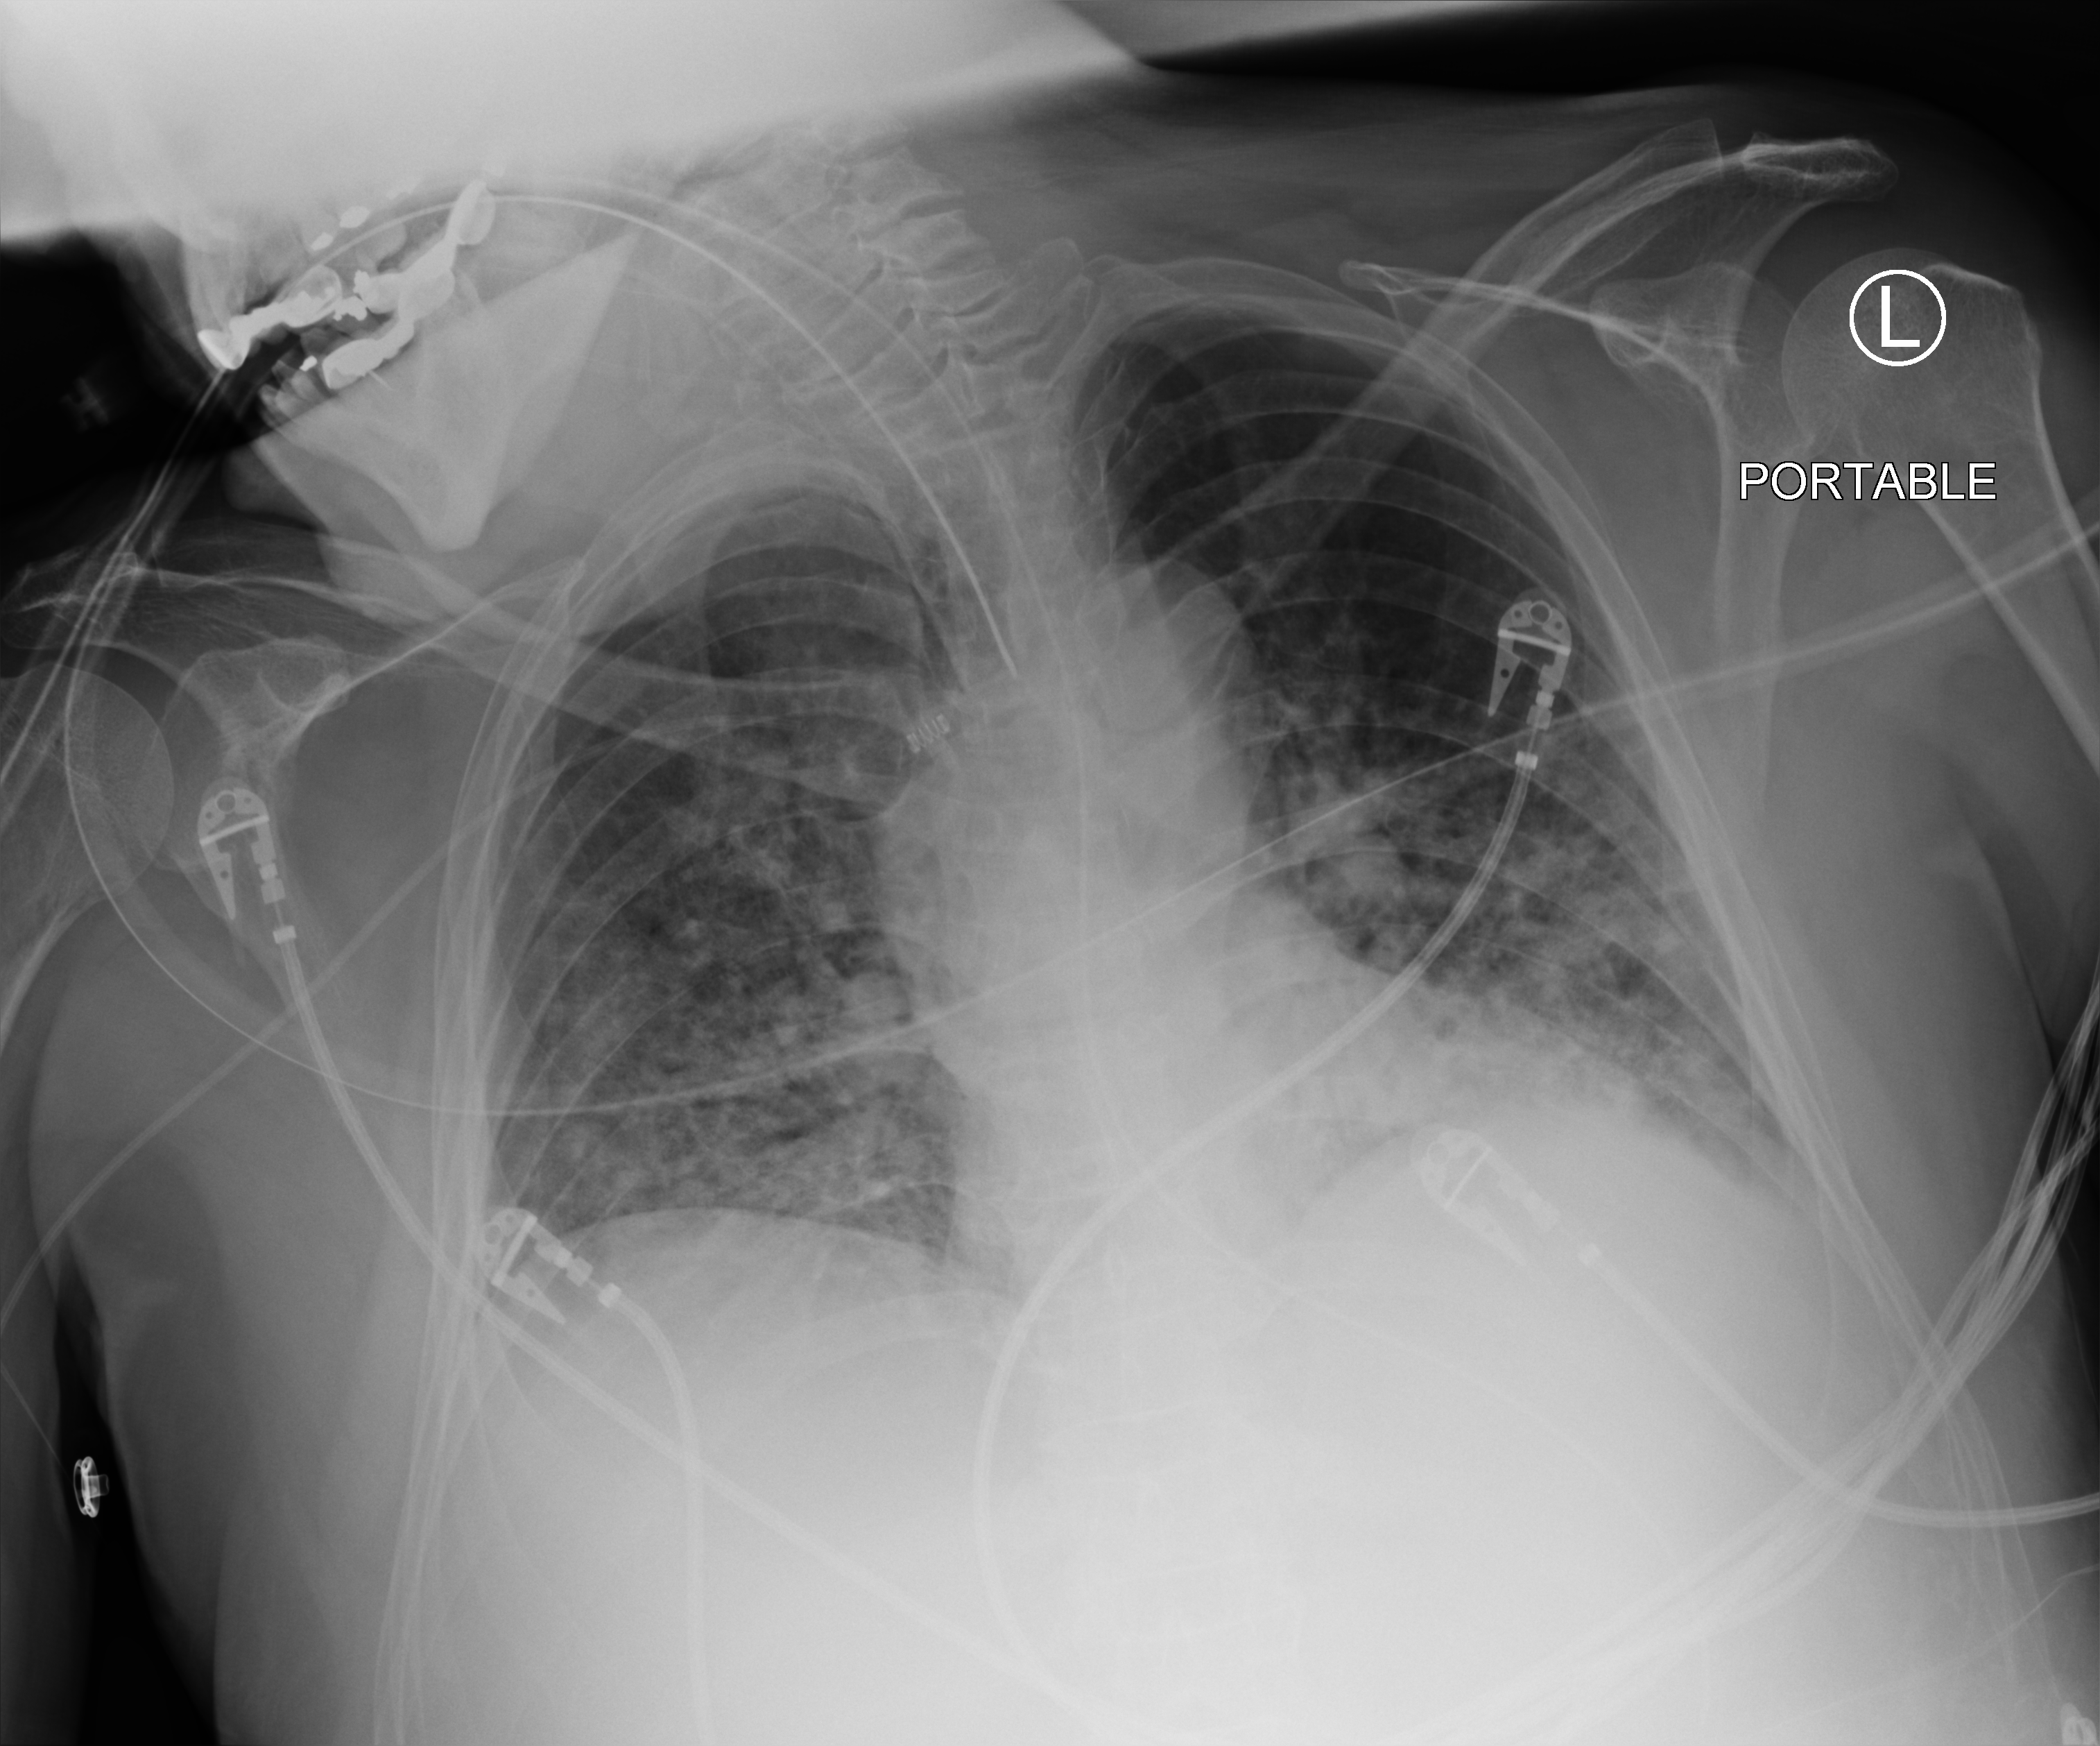
Portable chest radiograph, anteroposterior (AP) projection. Male patient hospitalised with COVID-19, age 60–74 years.
From the hospital-stay record, not from the radiograph (when in the stay this image was taken is not recorded):
- mechanically ventilated during this hospital stay: yes
- length of hospital stay: 19 days